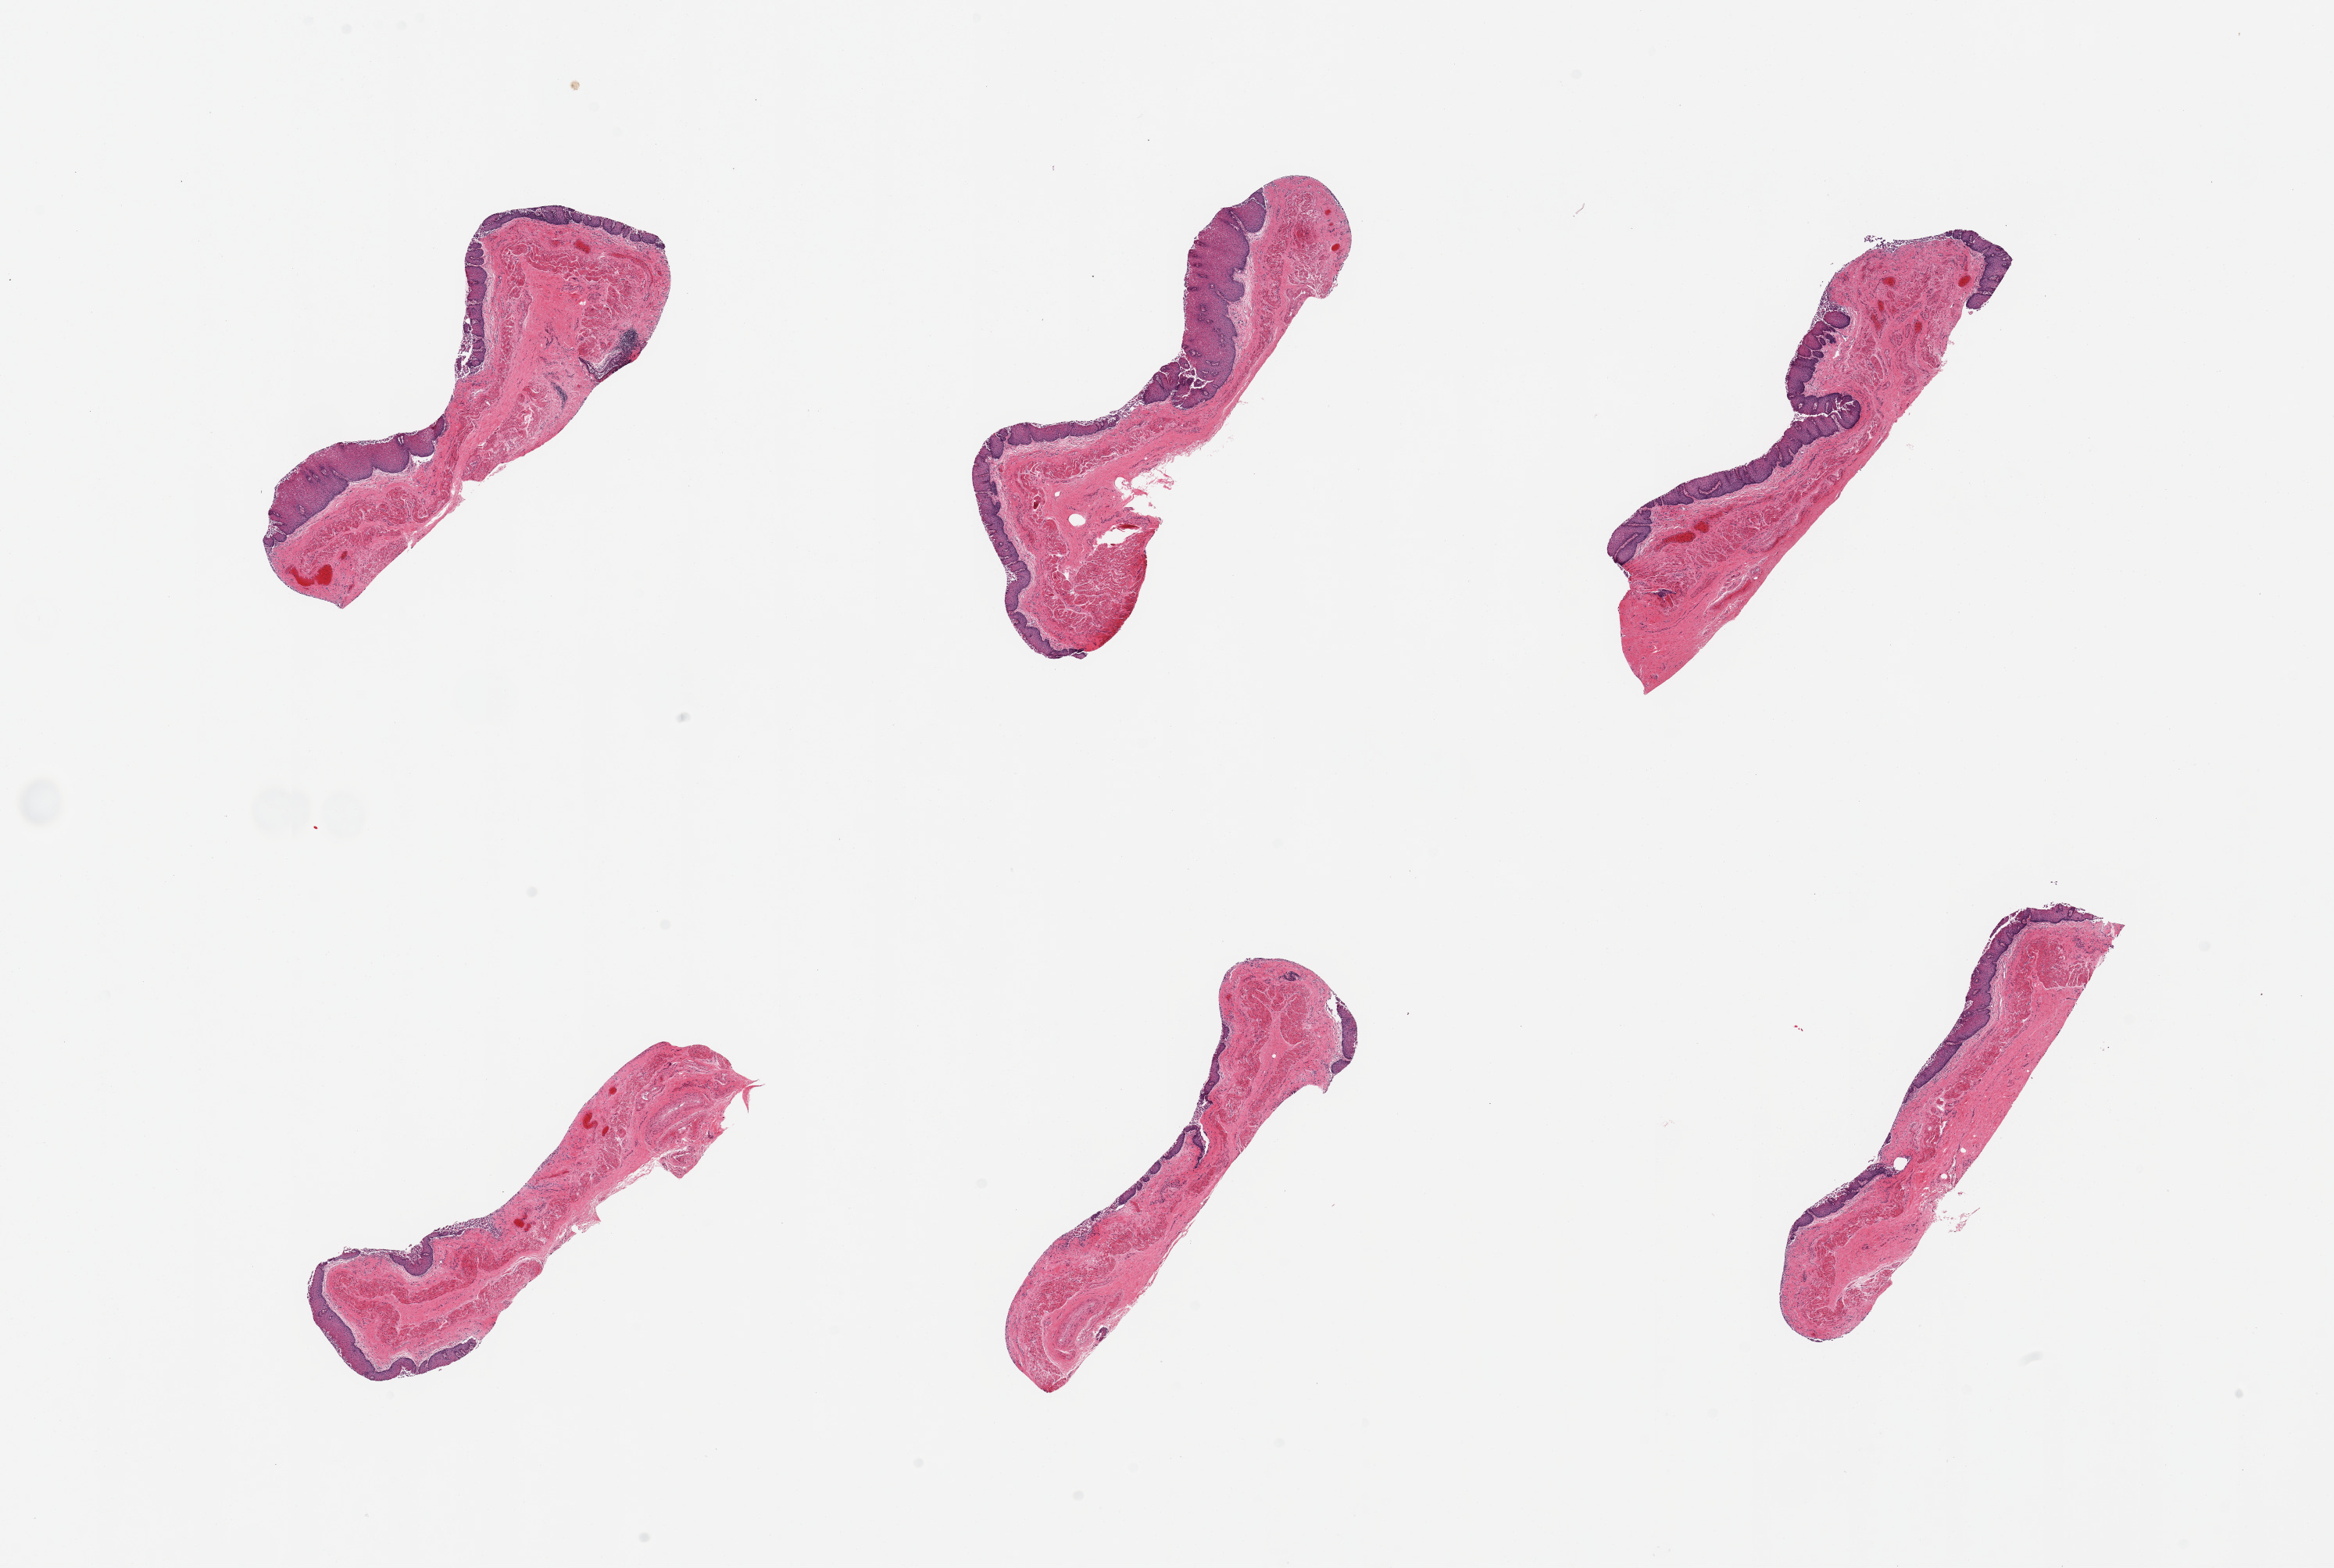
Digitized H&E-stained section — shown as a low-resolution overview of the whole scanned area (about 23.6 x 15.9 mm, slide scanned at 20x); PAXgene-fixed, paraffin-embedded tissue; sampled site (target tissue): esophageal mucous membrane; tissue donor sample. Male donor.
* review note (as recorded): 6 pieces; mucosa and muscularis mucosae present; focal epithelial sloughing